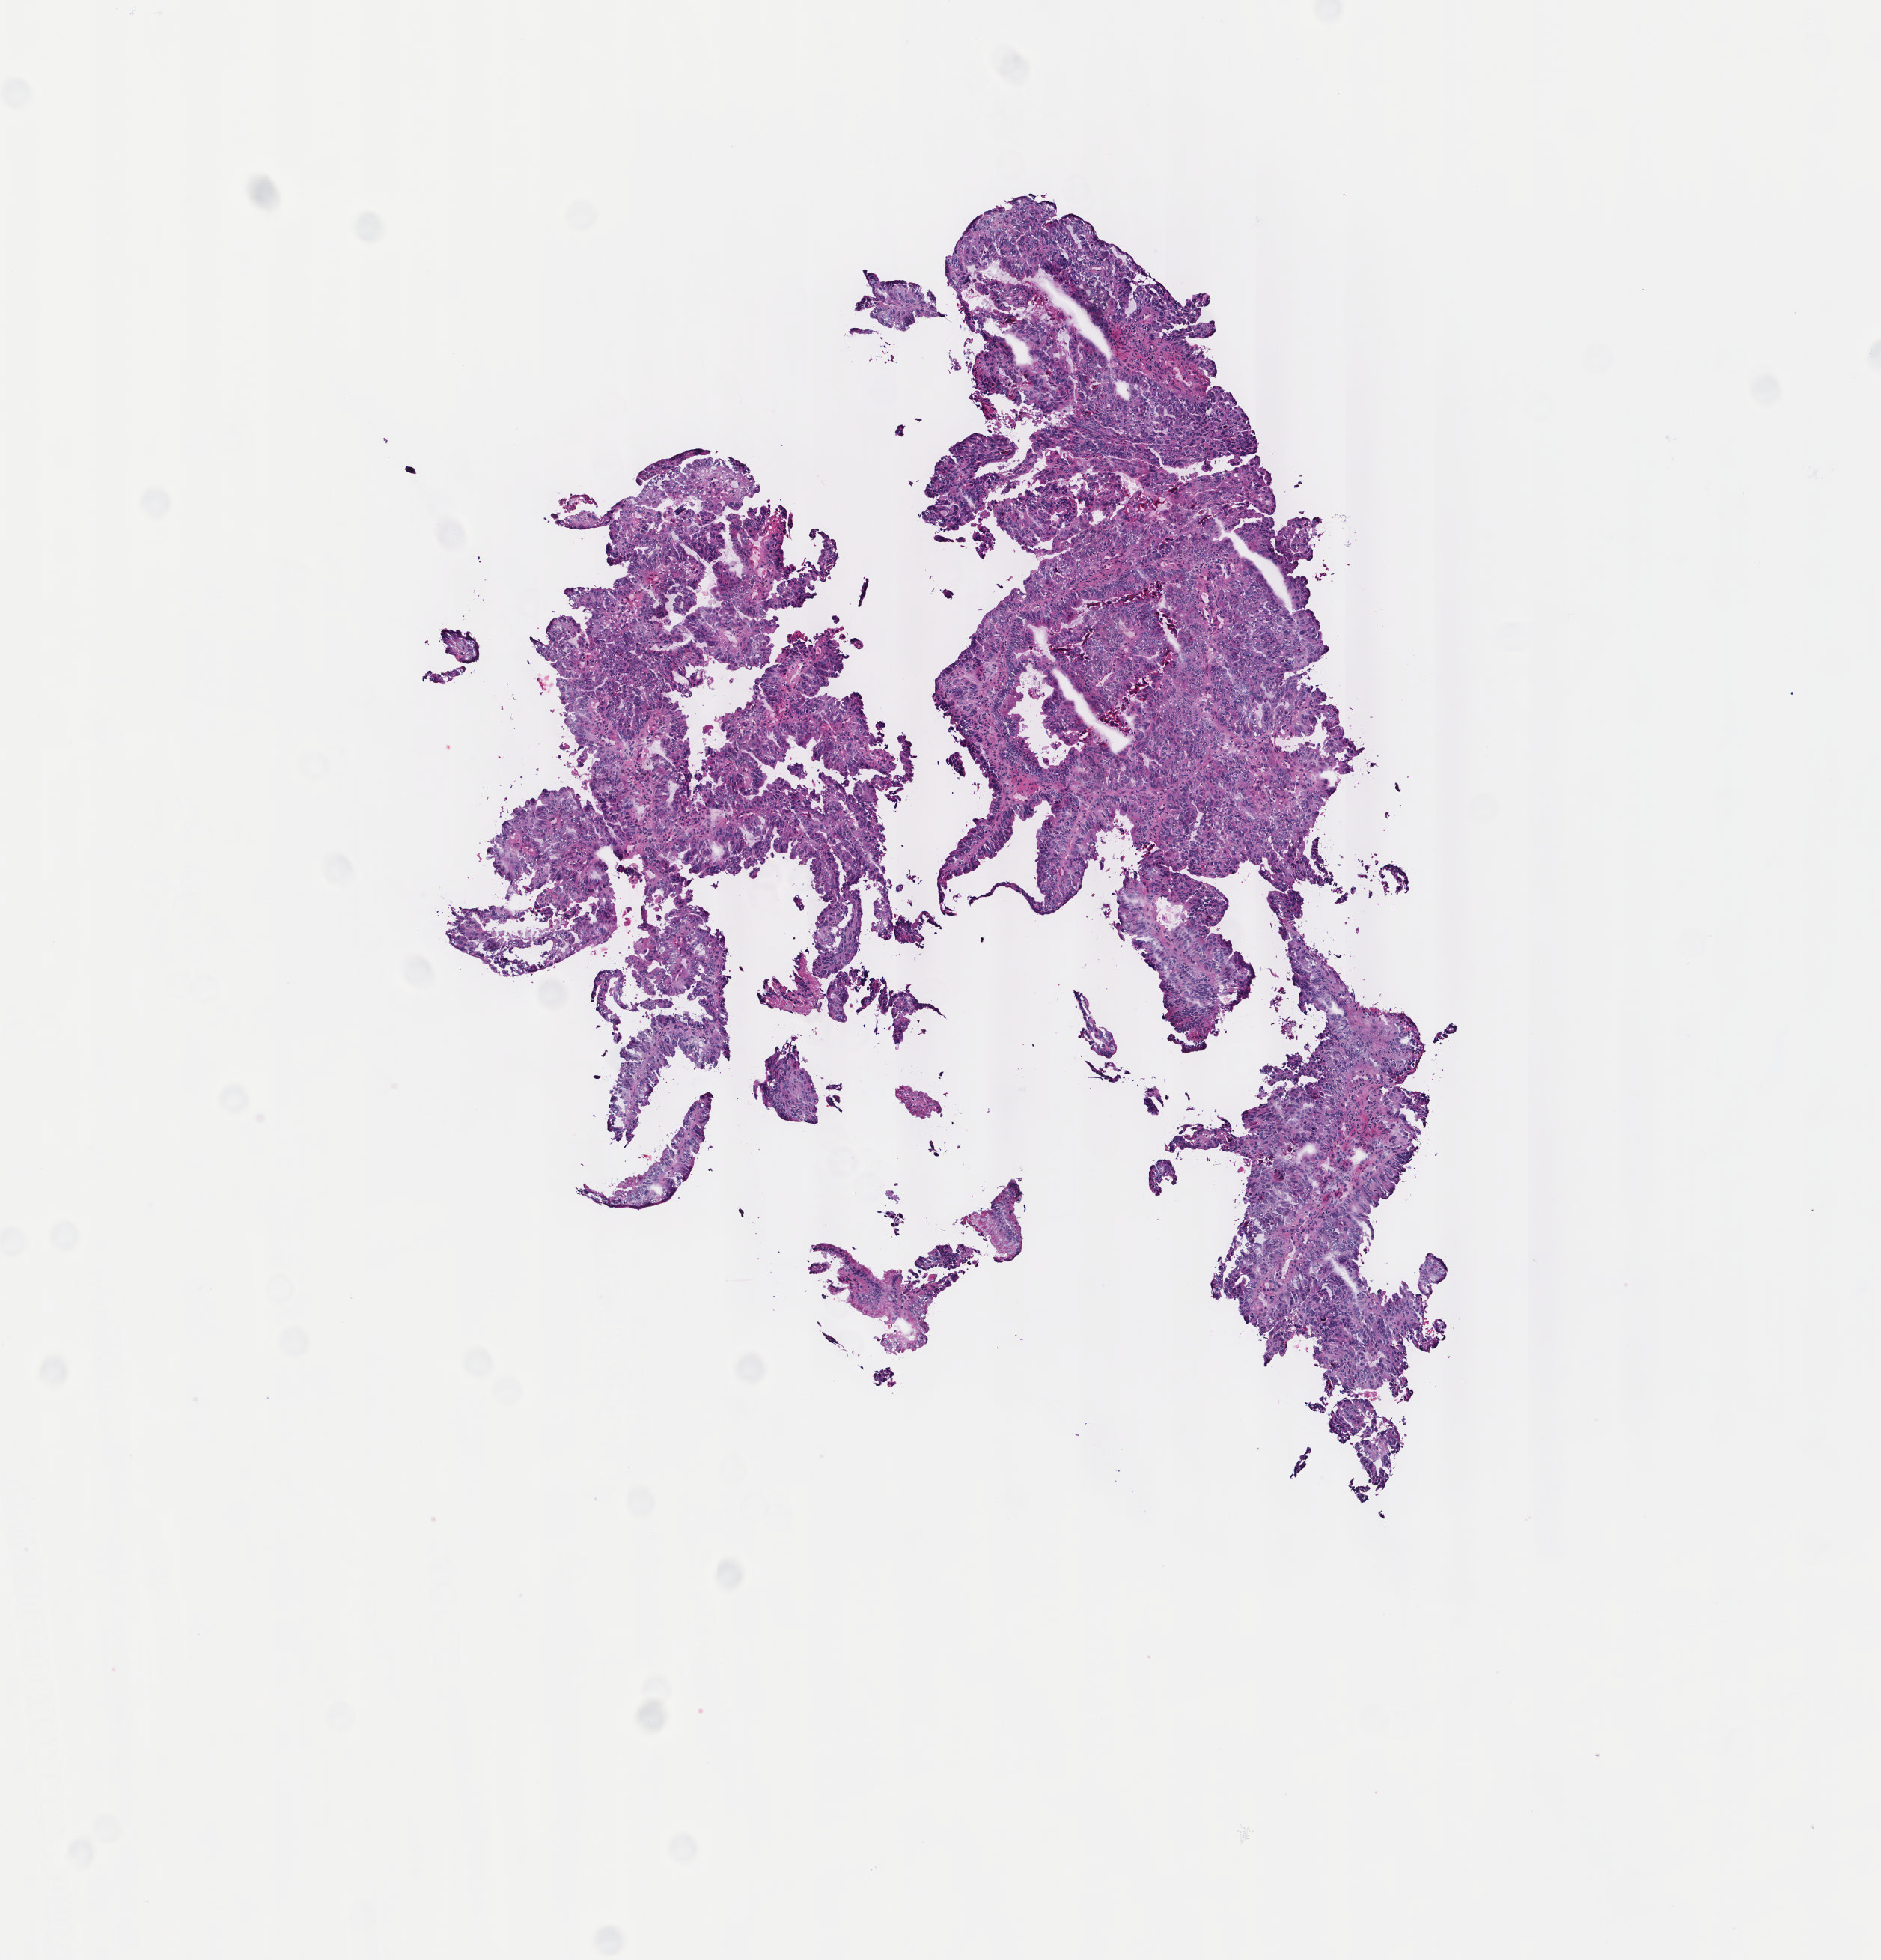
Whole-slide histology image, H&E — shown as a low-resolution overview of the whole scanned area (about 5.0 x 5.2 mm, acquisition: 40x scan); frozen section from the top of the tissue portion; sample: primary tumour, esophagus. Patient: male, age at initial diagnosis 45 years. Histologic grade: G2 (moderately differentiated). Slide review estimates, as recorded: tumour cells 85%, tumour nuclei 90%, normal cells 0%, stromal cells 15%, necrosis 0%. Inflammatory infiltration, as recorded: lymphocyte infiltration 4%, monocyte infiltration 2%, neutrophil infiltration 0%.
Diagnosis: Adenocarcinoma, NOS (middle third of esophagus). AJCC pathologic stage: IB.